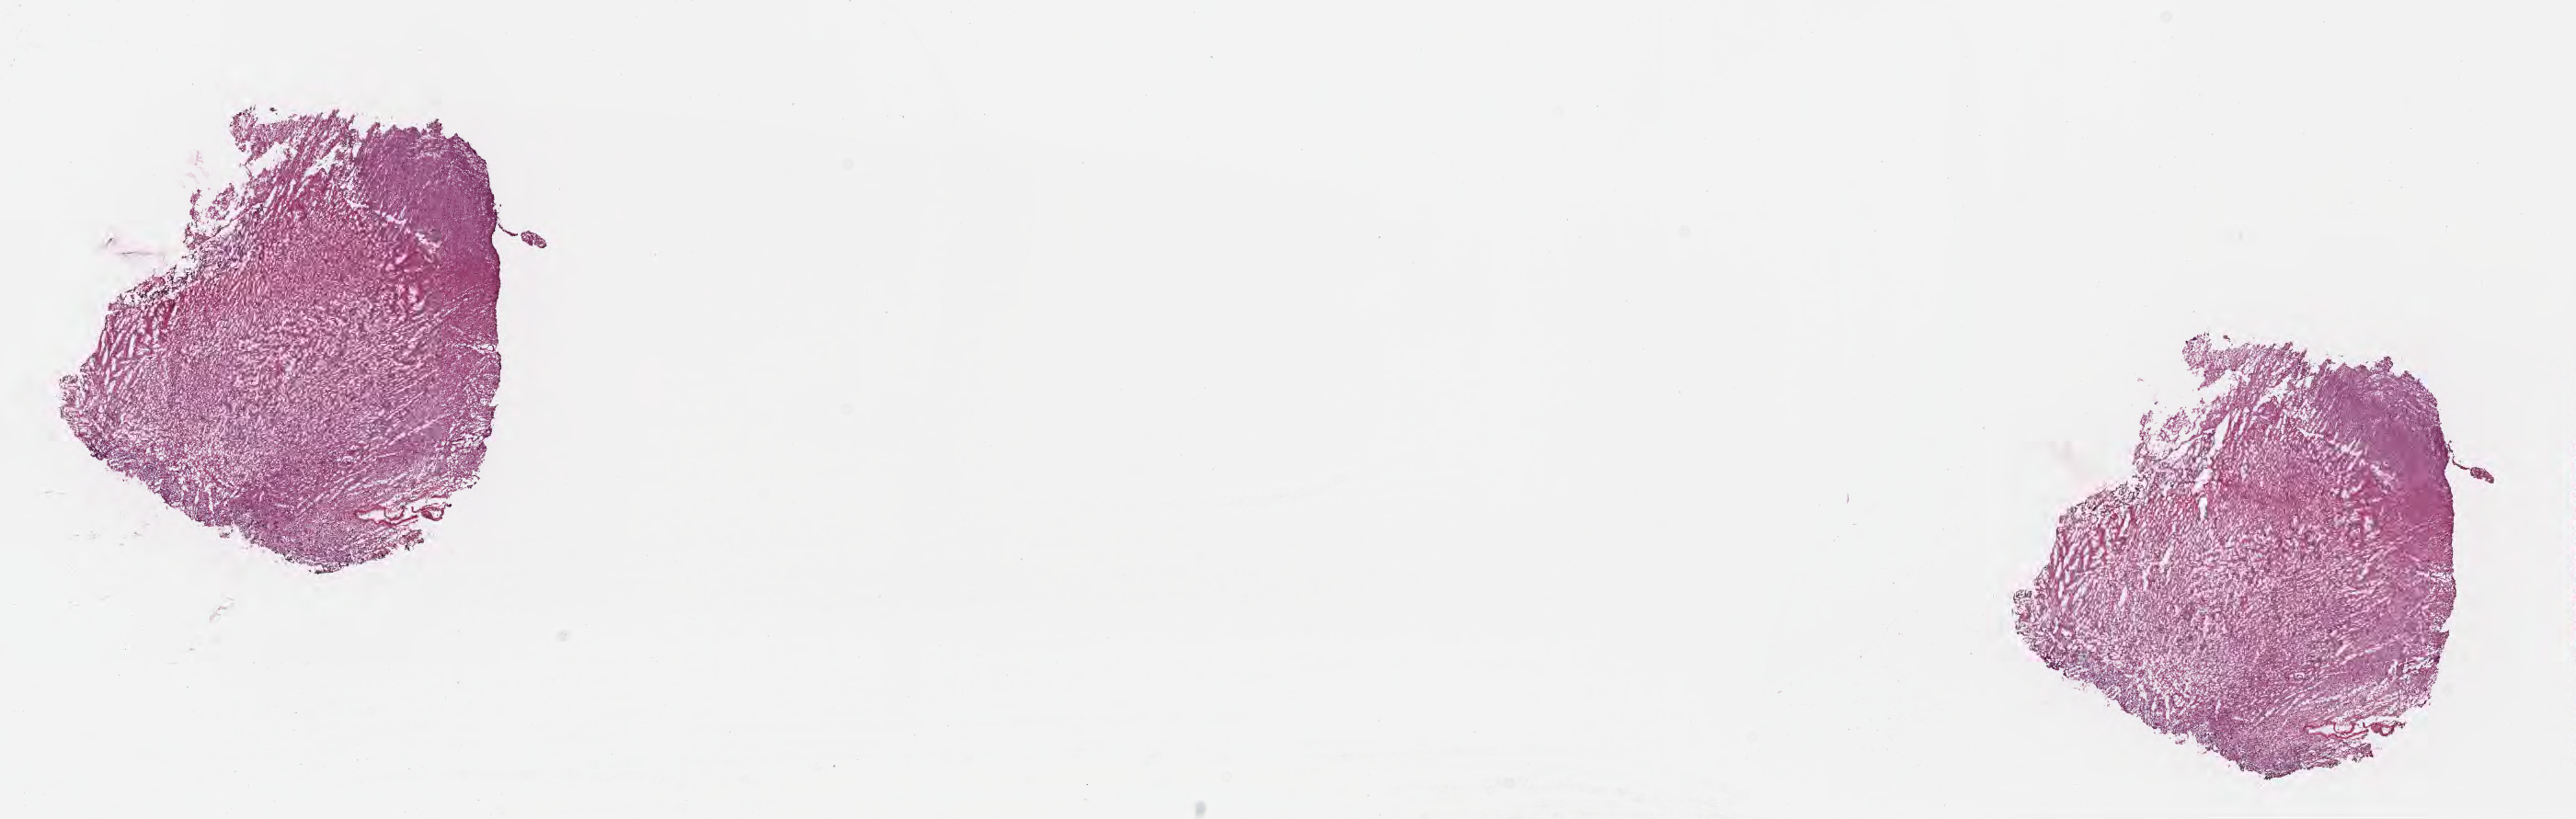
H&E whole-slide image, low-resolution overview of the scanned area, about 22.6 x 7.2 mm; frozen section; specimen: recurrent tumor; site: brain. Female patient; age at initial diagnosis 53 years. Composition of this section per pathologist review: tumor cells 20%, tumor nuclei 47%, stromal cells 56%, necrosis 2%, normal cells 22%. Inflammatory infiltration, as recorded: lymphocyte infiltration 1%, monocyte infiltration 0%, neutrophil infiltration 0%.
Patient diagnosis: Glioblastoma, NOS.